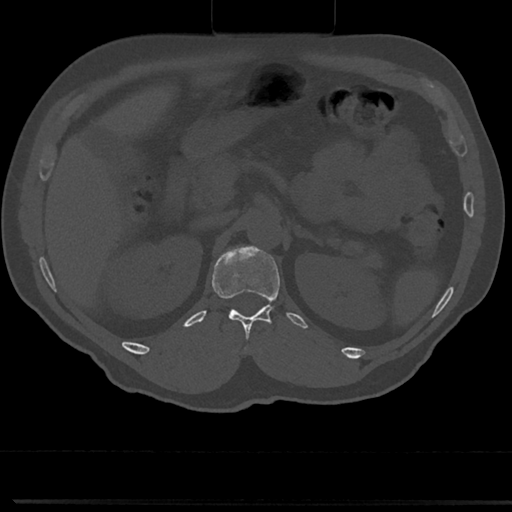
CT including the spine, one axial slice; slice 135 of 817 in the series (ordered by position); reconstruction kernel Br40s/3; 120 kVp; bone window (W 1800 / L 400 HU); 512 × 512 image matrix, field of view 355 × 355 mm. Male patient, age 61 years. Case-level facts recorded for this patient, not image findings: primary cancer: prostate.
Structures marked on this image (semi-automatically segmented with operator editing):
- T12 vertebra: bounding box (x1, y1, x2, y2) in pixels: (214, 262, 282, 357)